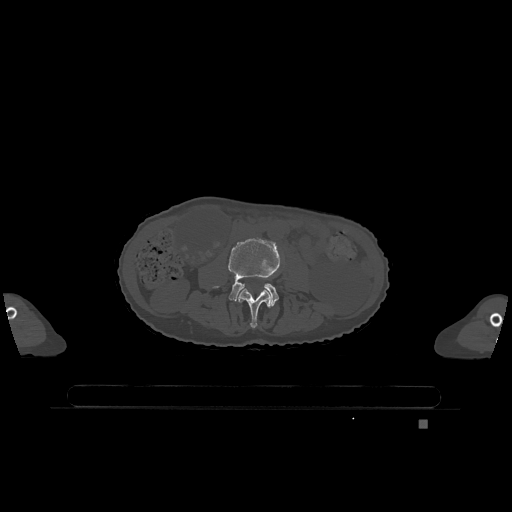
CT including the spine, one axial slice. Position 327 of 1317 along the scan axis. Bone window (W 1800 / L 400 HU). 0.5 mm slice thickness. 512 × 512 image matrix. Patient: female, 74 years. From the clinical record (not read from this slice): primary cancer: lung.
Annotated regions visible in this slice (semi-automatically segmented with operator editing):
- L3 vertebra: bounding box (x1, y1, x2, y2) in pixels: (238, 288, 271, 328)
- L4 vertebra: (214, 237, 280, 306)